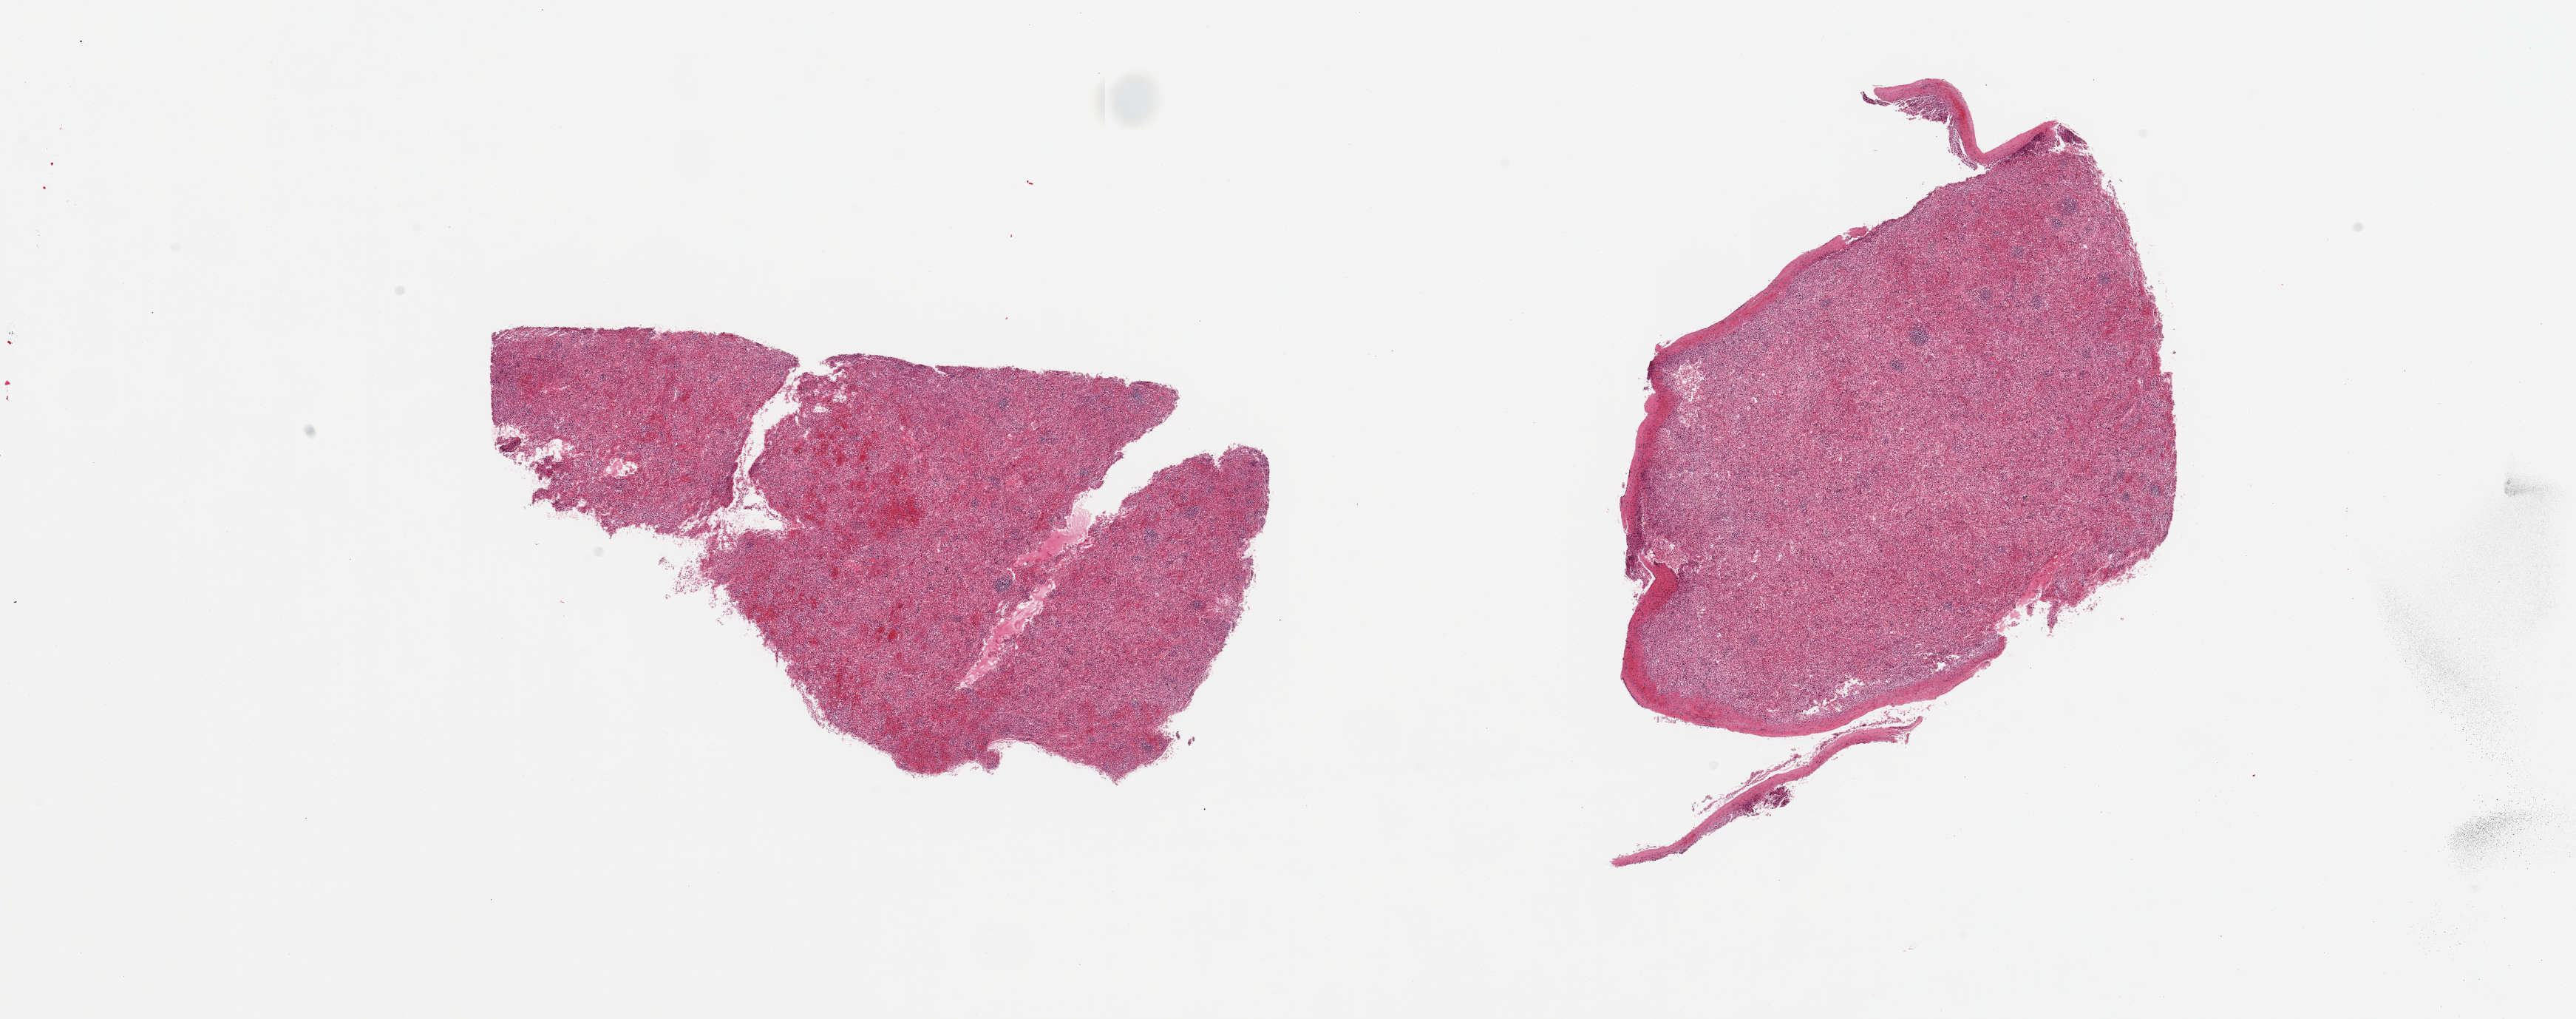
H&E whole-slide image, whole scanned area (about 27.6 x 10.9 mm, from a 20x scan) shown as a low-resolution overview; PAXgene-fixed, paraffin-embedded tissue; section of spleen (target tissue); donor tissue sample. Donor: male.
Reviewer comment on this tissue sample: 2 pieces; includes capsule (target is 5mm below capsule).